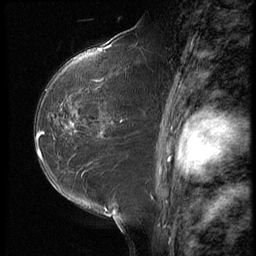
Breast MRI (dynamic contrast-enhanced), one sagittal slice. Position 39 of 64 along the scan axis. 3 images stored at this slice position (order not interpretable as contrast timing). 1.5 T. TE 4.2 ms, TR 9 ms. 2.5 mm slice thickness. 256 × 256 image matrix. Patient: female, 59 years. Case-level facts recorded for this patient, not image findings: setting: breast cancer imaged before/during neoadjuvant chemotherapy; receptor status: HER2-positive.
Outlined on this slice (semi-automatically segmented with operator editing):
- analysis volume of interest (the breast-tissue region the enhancement analysis was run in; not a lesion): box from (x=54, y=65) to (x=155, y=132) px
- tumour enhancement mask (voxels above the 140 % enhancement threshold inside the analysis volume of interest): (x=71, y=124)–(x=76, y=131)